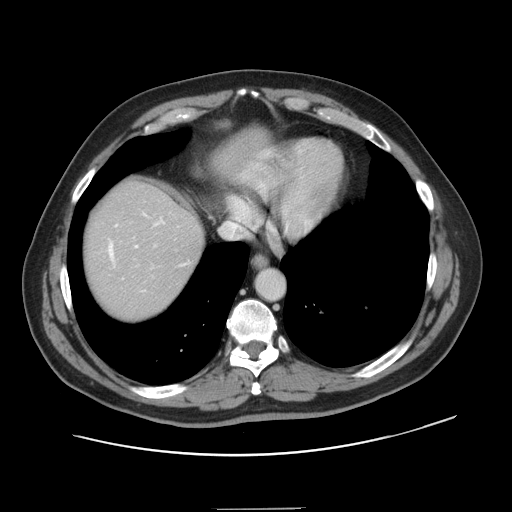
Contrast-enhanced abdominal CT, one axial slice. Slice 130 of 143 in the series (ordered by position). 120 kVp. Intravenous contrast given. Soft-tissue window (W 400 / L 40 HU). 2.5 mm slice thickness. 512 × 512 image matrix. Male patient, age 62 years. From the clinical record (not read from this slice): diagnosis: colorectal cancer liver metastases, imaged before liver resection; multiple liver metastases: yes; largest metastasis: 2.7 cm; disease in both lobes: no.
Outlined on this slice (outlined manually by an expert reader):
- hepatic veins: box from (x=109, y=215) to (x=184, y=266) px
- liver: (x=84, y=138)–(x=248, y=320)
- planned liver remnant (the part of the liver to remain after resection): (x=84, y=182)–(x=204, y=300)